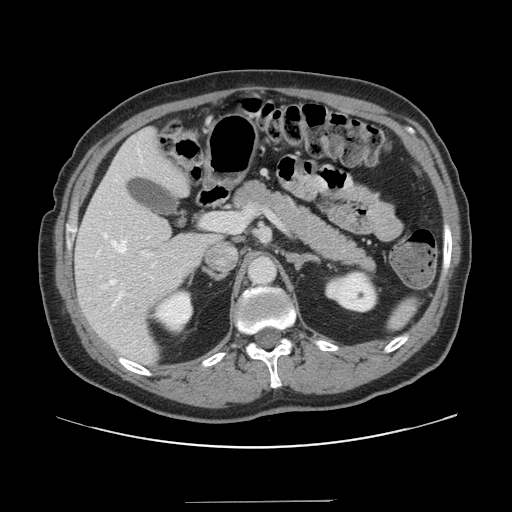
Contrast-enhanced abdominal CT, one axial slice; slice 85 of 151 in the series (ordered by position); 120 kVp; soft-tissue window (W 400 / L 40 HU); 2.5 mm slice thickness; 512 × 512 image matrix, field of view 399 × 399 mm. Male patient, age 63 years. From the clinical record (not read from this slice): diagnosis: colorectal cancer liver metastases, imaged before liver resection; multiple liver metastases: no; largest metastasis: 2.1 cm.
Structures marked on this image (manually delineated by an expert):
- hepatic veins: bounding box [x1, y1, x2, y2] px = [104, 161, 142, 331]
- liver: [76, 130, 217, 365]
- planned liver remnant (the part of the liver to remain after resection): [76, 130, 217, 365]
- portal vein (with intrahepatic branches): [141, 210, 252, 257]